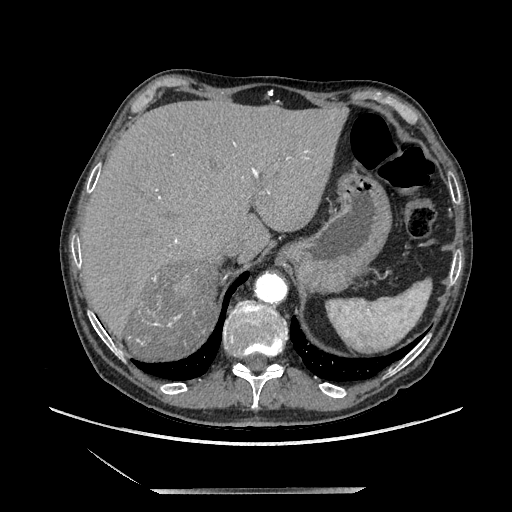
Contrast-enhanced abdominal CT, one axial slice; slice 168 of 243 in the series (ordered by position); soft-tissue window (W 400 / L 40 HU); 1.25 mm slice thickness; 512 × 512 image matrix, field of view 420 × 420 mm. Male patient. From the clinical record (not read from this slice): diagnosis: adrenocortical carcinoma; tumour side: right adrenal; tumour size at pathology: 16 cm; Ki-67 index: 17 %; stage (as recorded): 3.
Annotated regions visible in this slice (semi-automatically segmented with operator editing):
- mass: bounding box (x1, y1, x2, y2) in pixels: (127, 268, 220, 358)